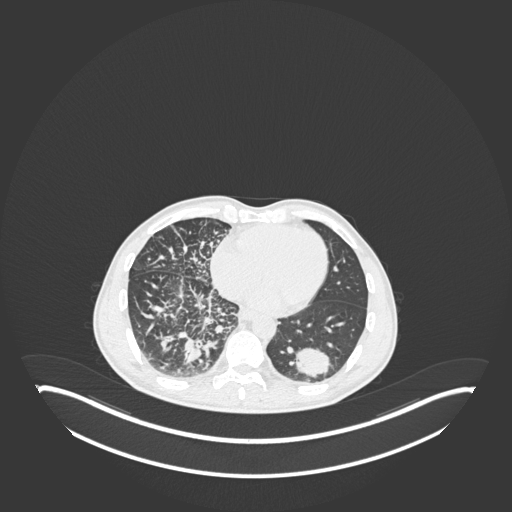
Chest CT, one axial slice. 120 kVp. Lung window (W 1500 / L -600 HU). 512 × 512 image matrix. Male patient, age 49 years. From the clinical record (not read from this slice): clinical TNM (as recorded): T2b N1 M0.
Structures marked on this image (bounding box drawn by a radiologist):
- lung tumour (recorded histology: adenocarcinoma): bounding box [x1, y1, x2, y2] px = [291, 346, 333, 382]